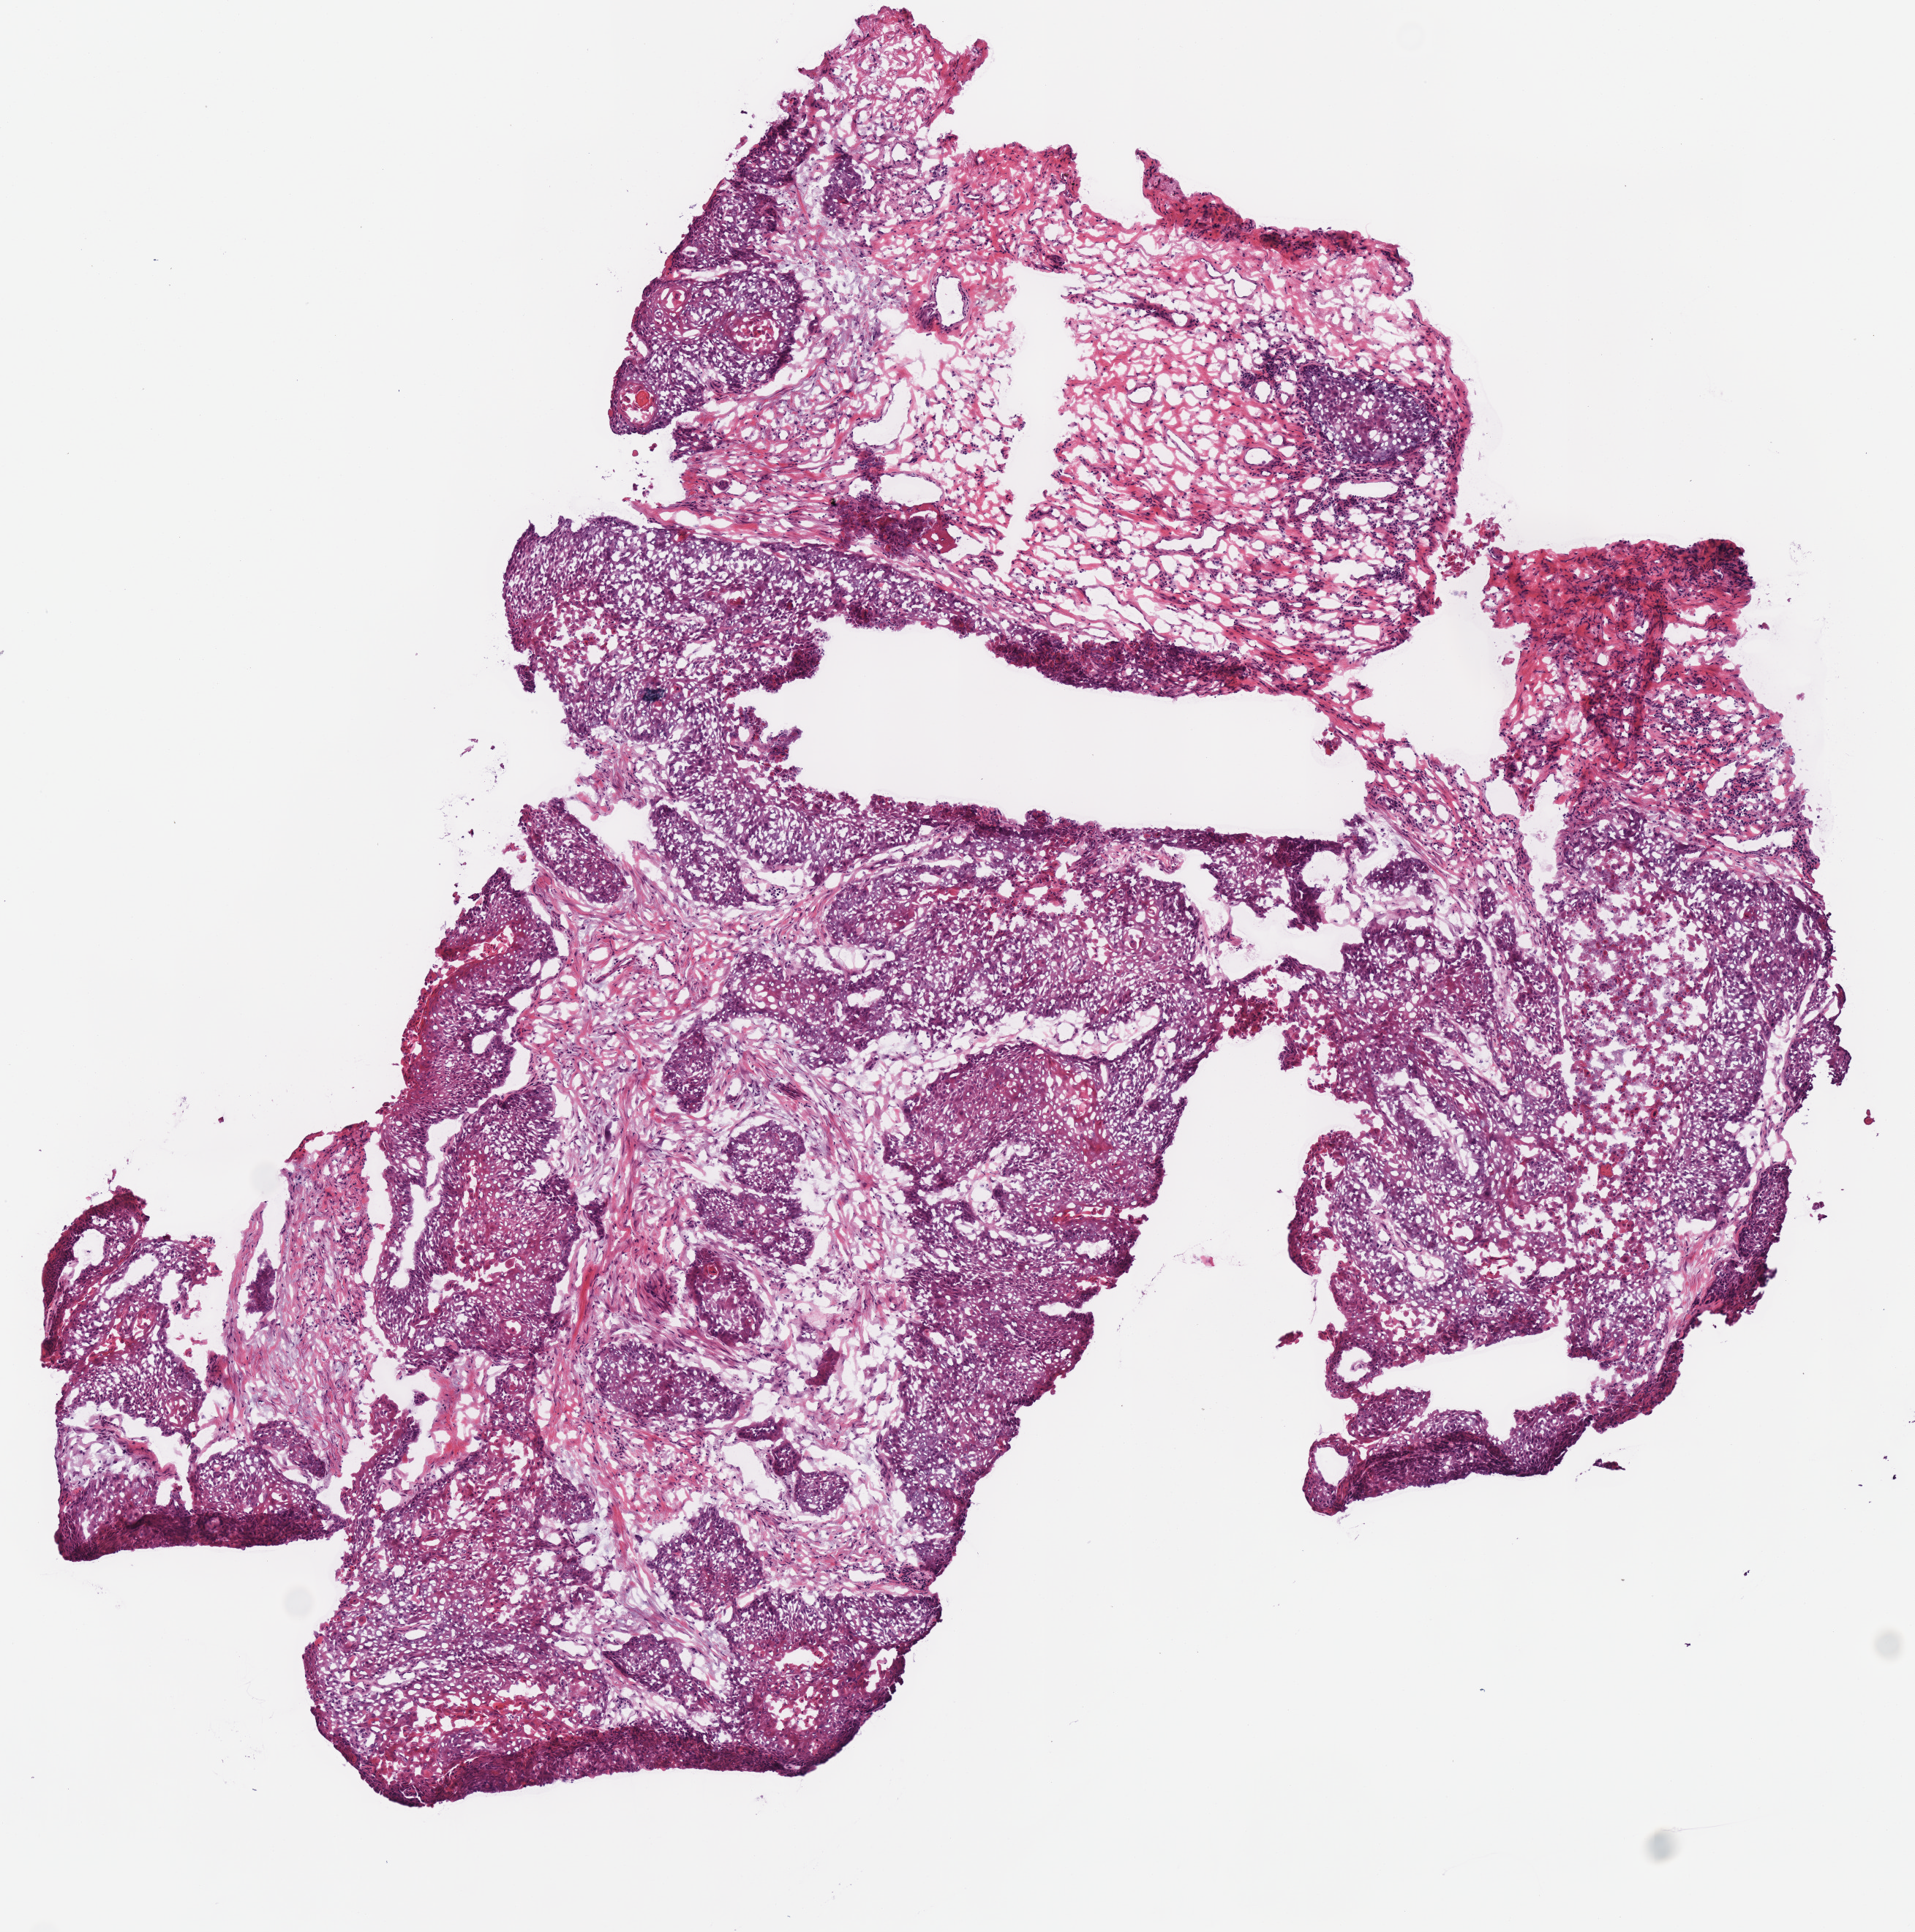
Hematoxylin and eosin (H&E) stained whole-slide image — whole scanned area (about 5.2 x 5.2 mm, acquisition: 40x scan) shown as a low-resolution overview. Frozen section. Head and neck, primary tumour sample. Patient: male, age at initial diagnosis 56 years. Histologic grade: G2 (moderately differentiated). Pathologist review of this section (percent, as recorded): tumour cells 75%, tumour nuclei 75%, normal cells 0%, stromal cells 25%, necrosis 0%.
TNM: T4a N0. Pathologic diagnosis: Squamous cell carcinoma, NOS (larynx, NOS). AJCC pathologic stage: IVA (7th edition). Laterality: left.